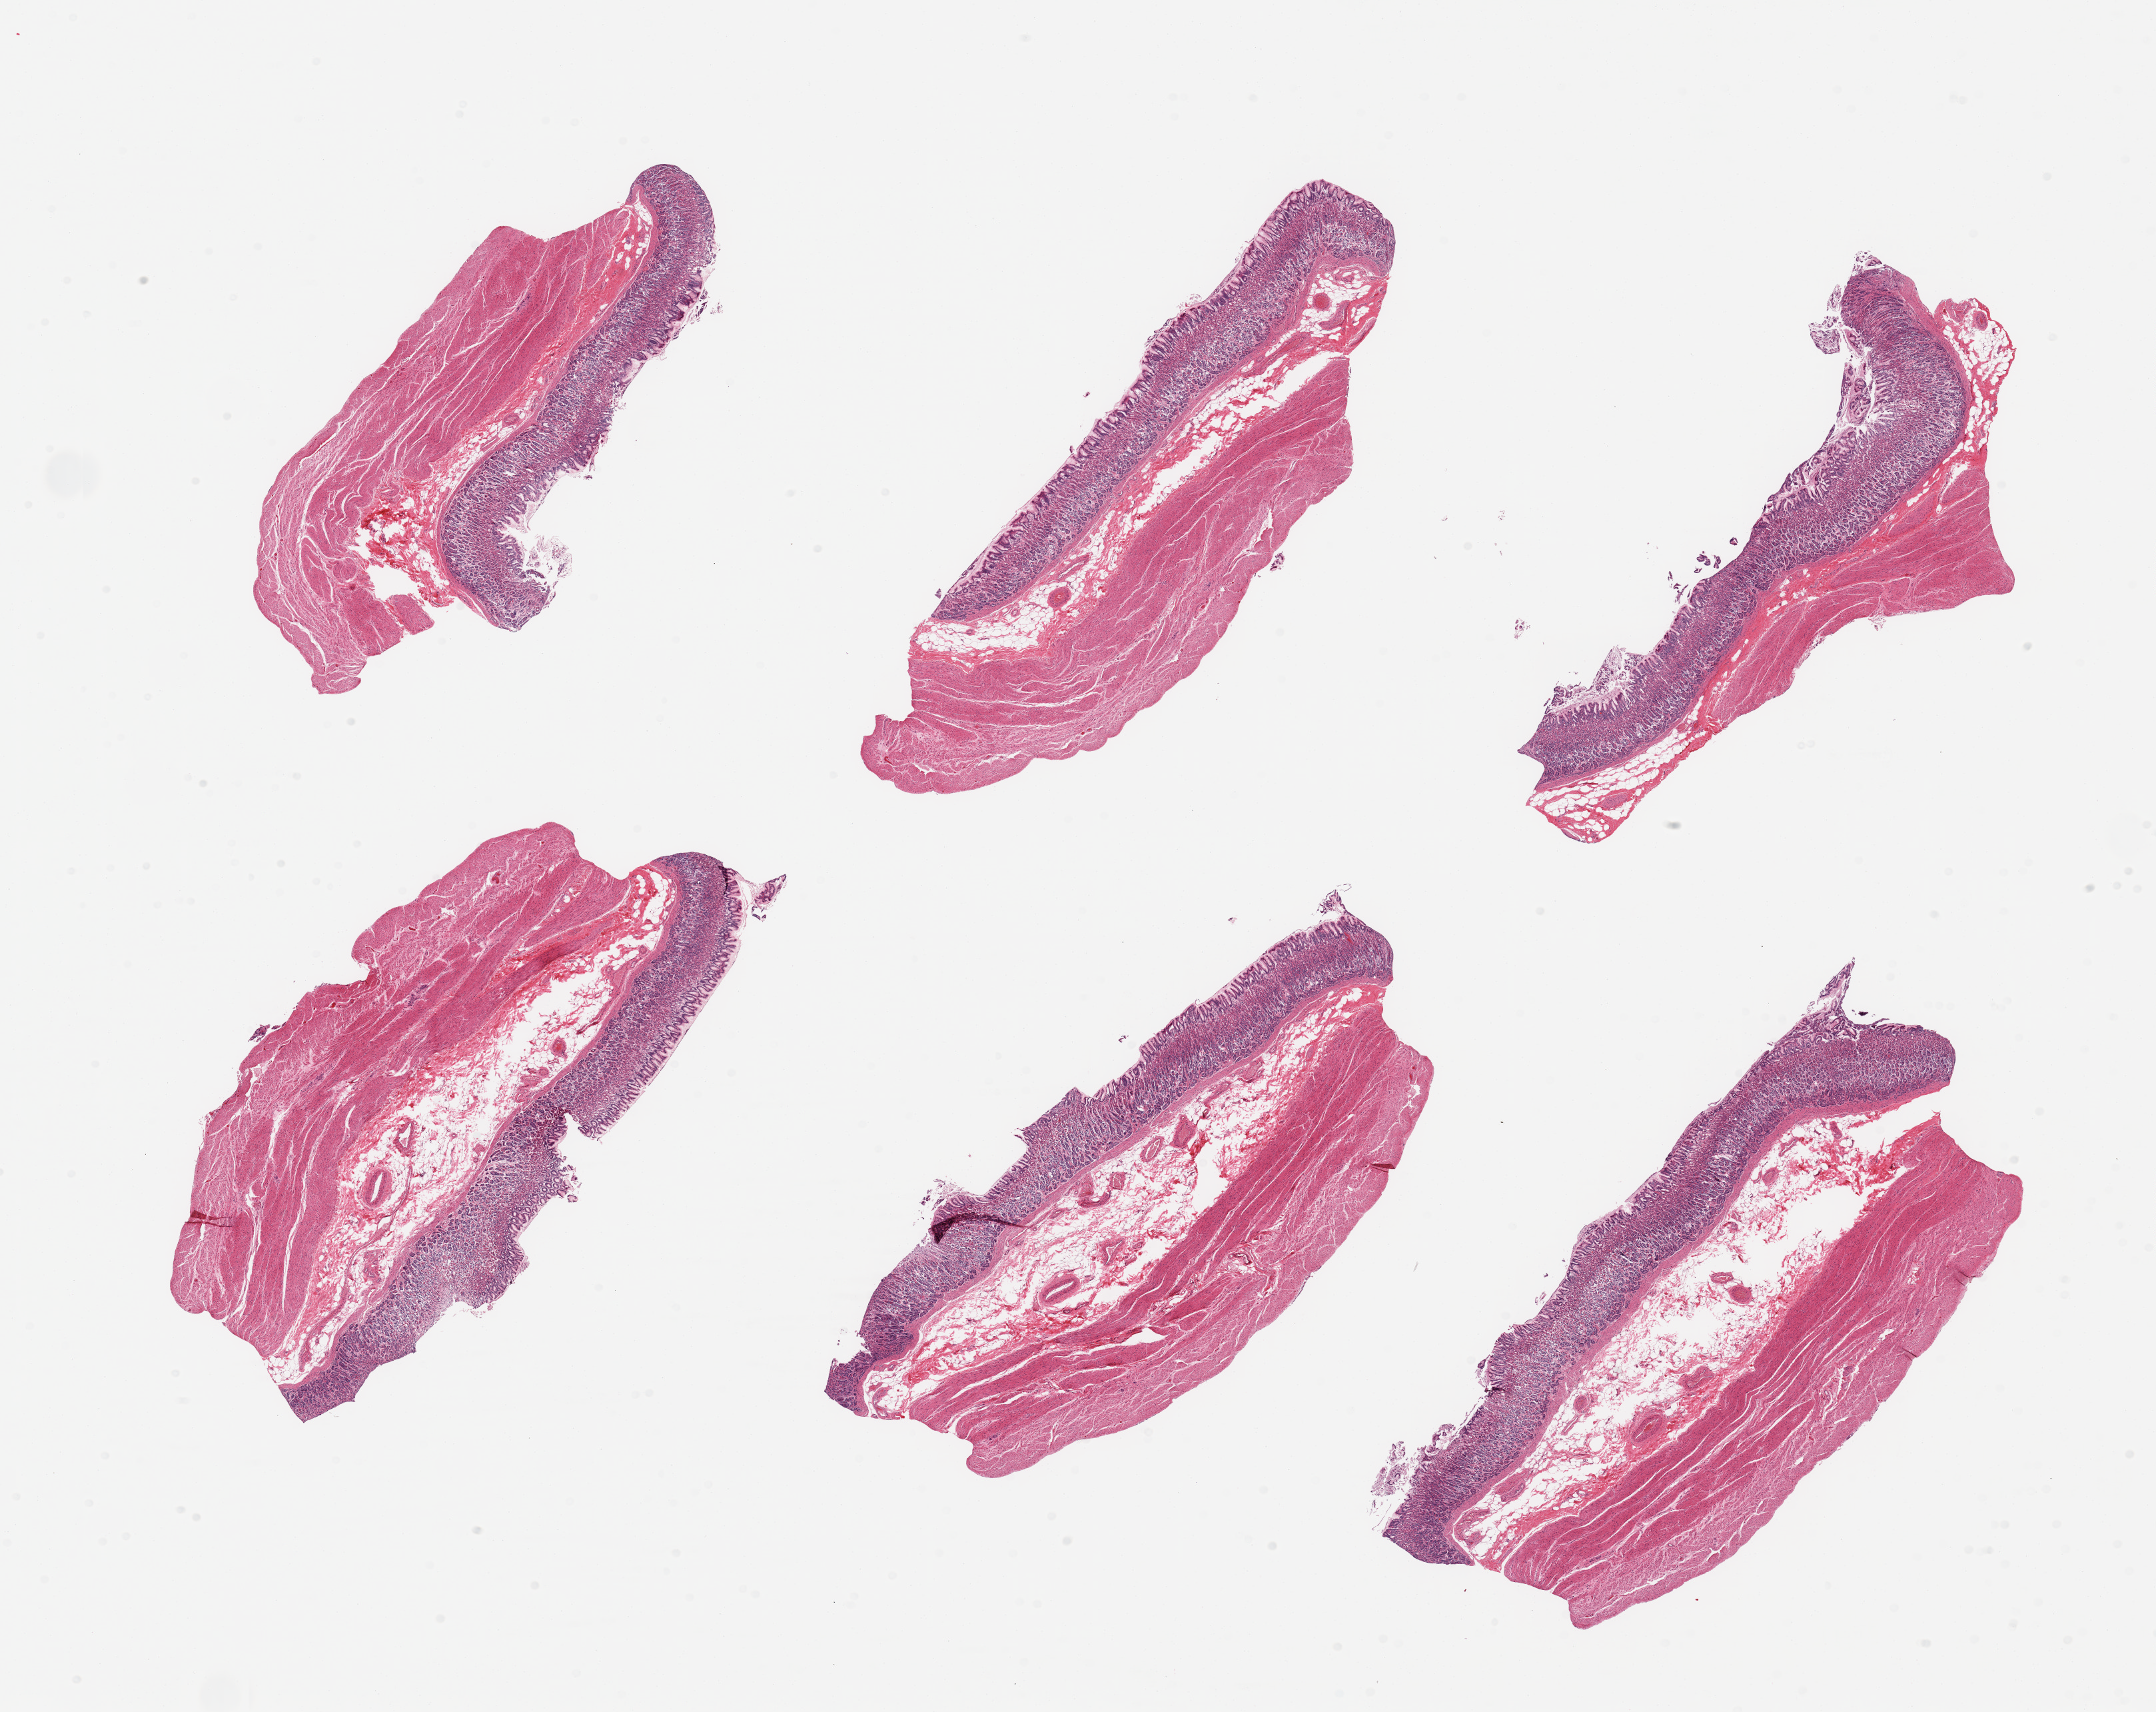
Hematoxylin and eosin (H&E) whole-slide image — whole scanned area (about 25.6 x 20.3 mm) shown as a low-resolution overview. PAXgene-fixed, paraffin-embedded tissue. Target tissue: stomach. Donor tissue sample. Male donor.
• reviewer comment on this tissue sample: 6 pieces; full thickness